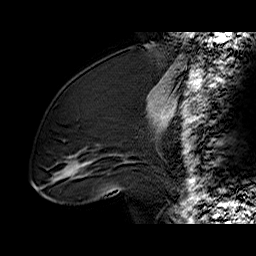
Breast MRI (dynamic contrast-enhanced), one sagittal slice; dynamic contrast-enhanced series, time point 2 of 6 at this slice position (early post-contrast); 1.5 T; TE 6.2 ms, TR 32.4 ms; 4 mm slice thickness; 256 × 256 image matrix. Female patient. Case-level facts recorded for this patient, not image findings: setting: breast cancer imaged before/during neoadjuvant chemotherapy; receptor status: triple-negative.
Structures marked on this image (semi-automatic segmentation, software-assisted and operator-edited):
- analysis volume of interest (the breast-tissue region the enhancement analysis was run in; not a lesion): bounding box <36,97,134,196> (left, top, right, bottom; pixels)
- tumour enhancement mask (voxels above the 100 % enhancement threshold inside the analysis volume of interest): <125,162,130,163>